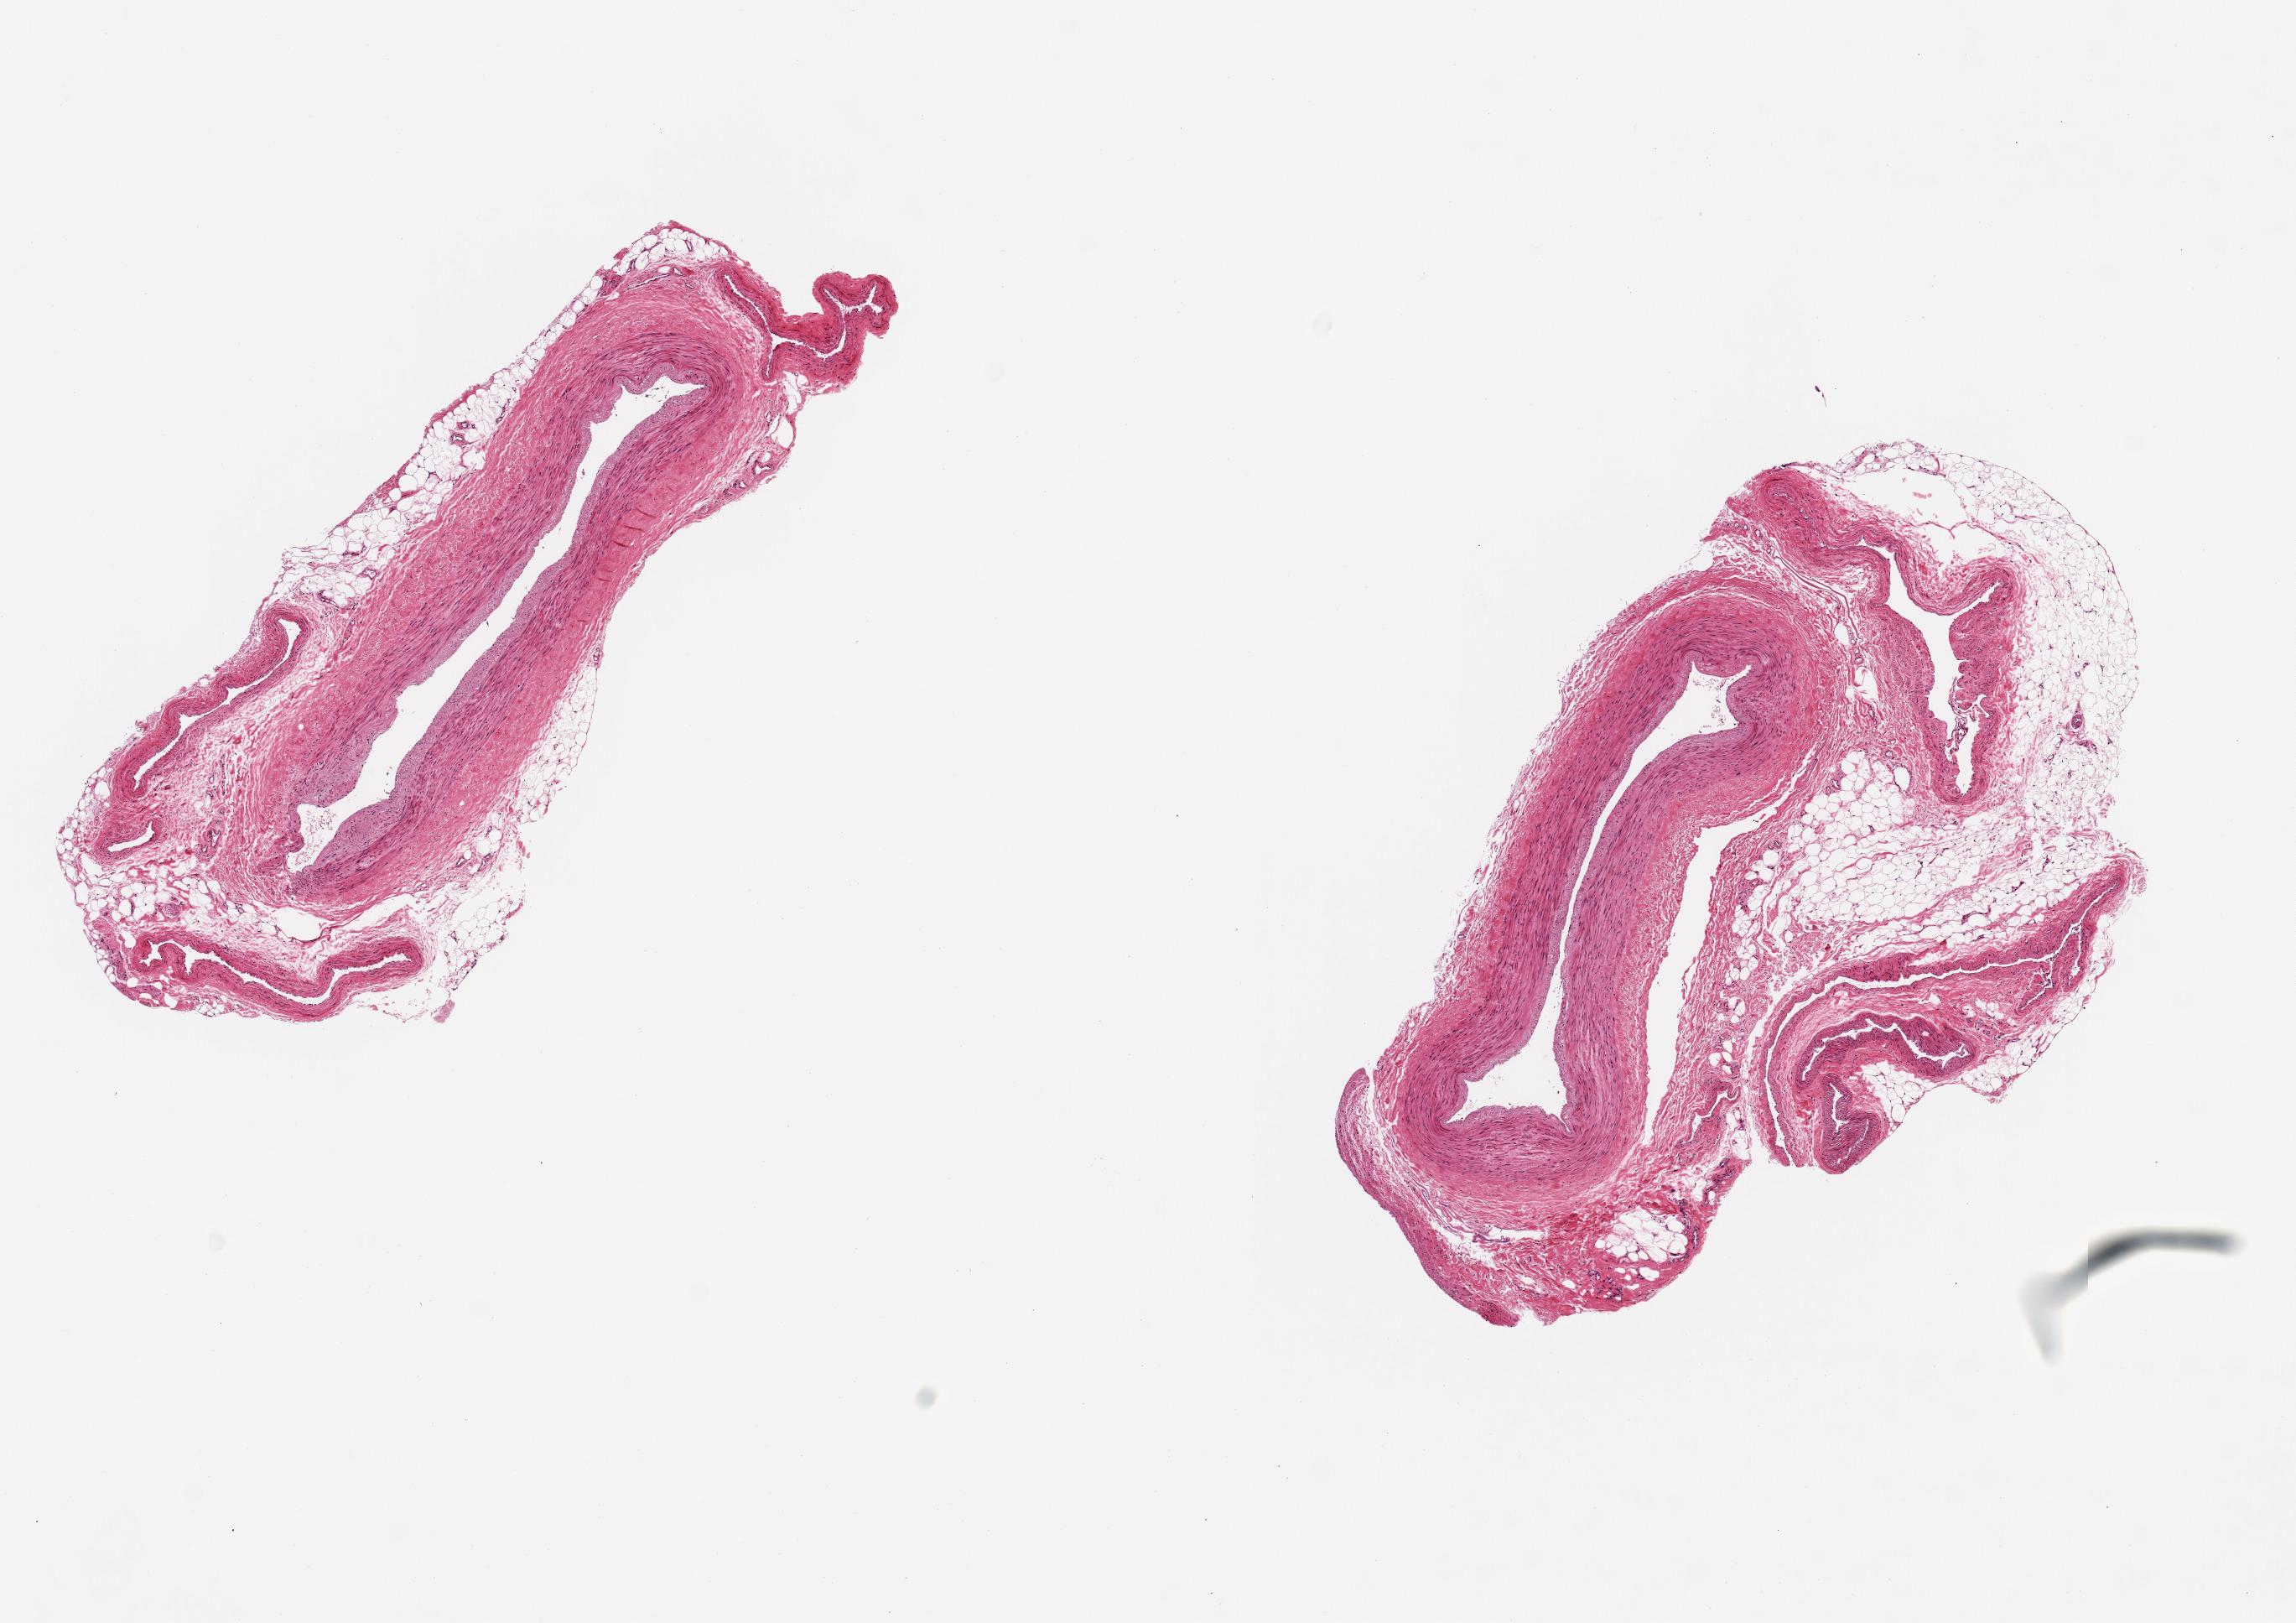
Hematoxylin and eosin (H&E) whole-slide image, brightfield, low-resolution overview of the scanned area, about 10.8 x 7.7 mm (slide scanned at 20x). PAXgene-fixed paraffin-embedded (PFPE) section. Section of tibial artery (target tissue). Tissue donor sample. Donor: male.
* pathologist's review note for this sample: 2 3x1mm aliquots, surrounded in to or part by up to 2mm rim of fat, small vessels & connective tissue